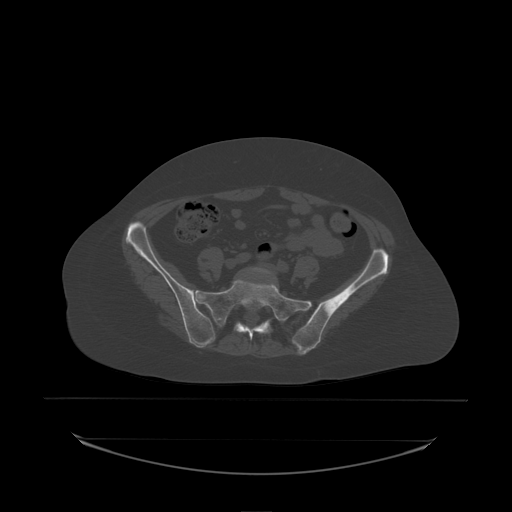
CT including the spine, one axial slice. Bone window (W 1800 / L 400 HU). 2.5 mm slice thickness. 512 × 512 image matrix, field of view 500 × 500 mm. Patient: female, 53 years. Case-level facts recorded for this patient, not image findings: primary cancer: lung; vertebrae with lytic lesions (as recorded): T7, L1.
Structures marked on this image (semi-automatic segmentation, software-assisted and operator-edited):
- L5 vertebra: box from (x=253, y=268) to (x=275, y=279) px